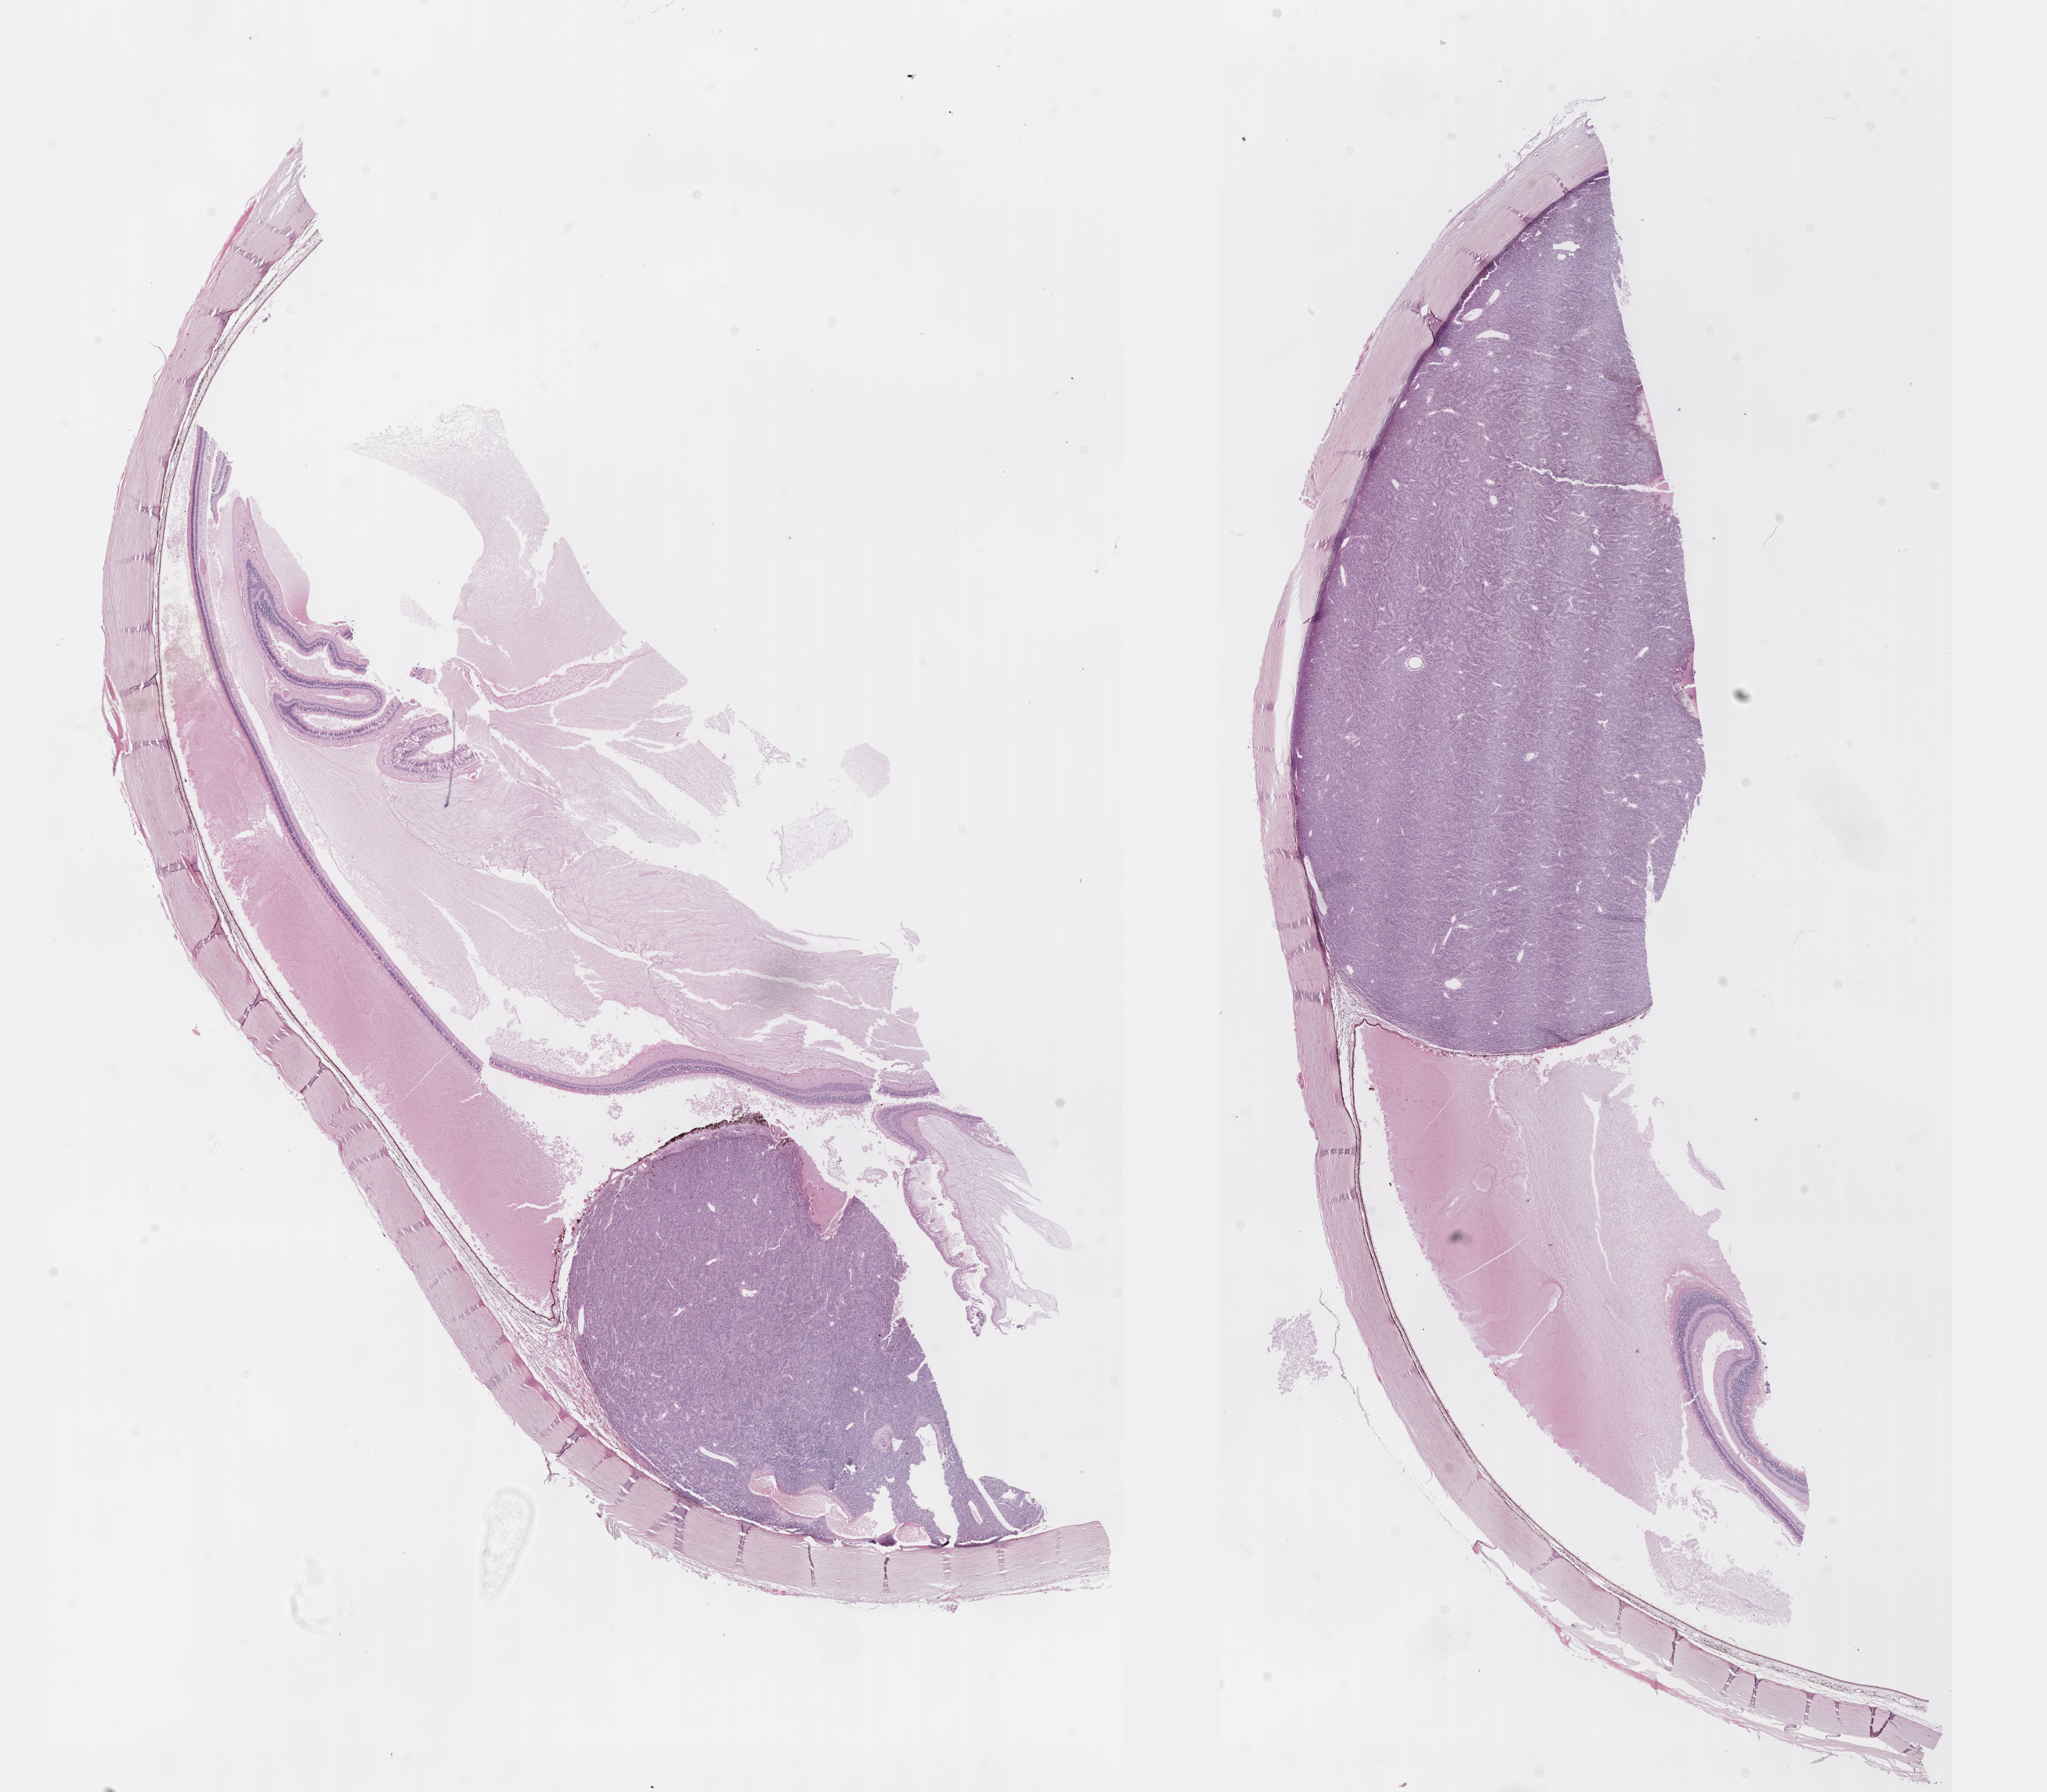
Whole-slide histology image, Hematoxylin and eosin (H&E) stained — low-resolution overview of the scanned area, about 21.1 x 18.5 mm (slide scanned at 40x), formalin-fixed paraffin-embedded (FFPE) diagnostic section, uvea, primary tumour sample. Male, age 45 years at initial diagnosis.
Pathologic diagnosis: Spindle cell melanoma, NOS (ciliary body). AJCC pathologic stage: IIIA (7th edition). TNM: T3b N0 M0.